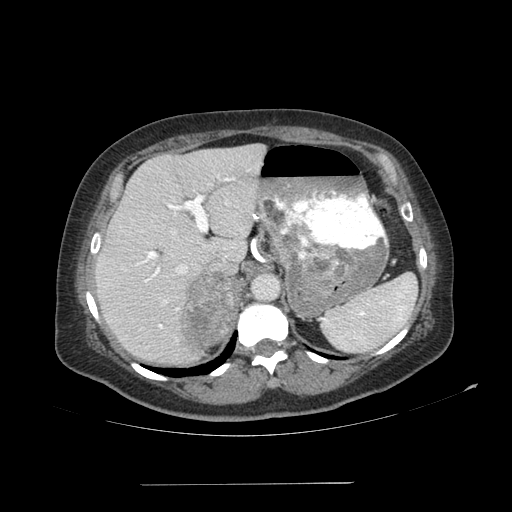
Contrast-enhanced abdominal CT, one axial slice. Reconstruction kernel SOFT. 120 kVp. Soft-tissue window (W 400 / L 40 HU). 2.5 mm slice thickness. 512 × 512 image matrix. Patient: female, 67 years. From the clinical record (not read from this slice): diagnosis: adrenocortical carcinoma; tumour side: right adrenal; tumour size at pathology: 9.8 cm; Ki-67 index: 59 %; stage (as recorded): 4.
Structures marked on this image (semi-automatically segmented with operator editing):
- mass: bounding box <182,274,237,347> (left, top, right, bottom; pixels)